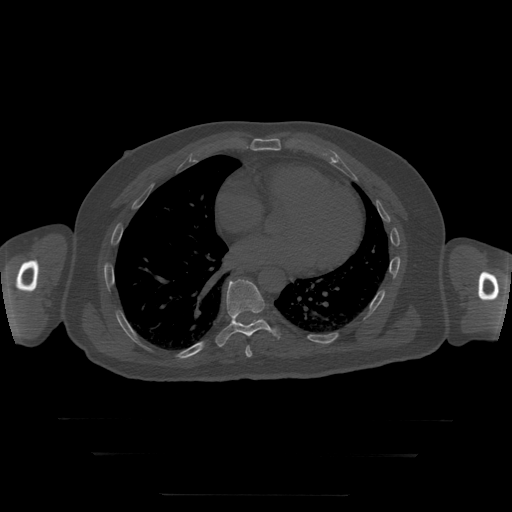
CT including the spine, one axial slice. Slice 145 of 397 in the series (ordered by position). Reconstruction kernel STANDARD. 120 kVp. Bone window (W 1800 / L 400 HU). 512 × 512 image matrix. Patient age 73 years. Case-level facts recorded for this patient, not image findings: primary cancer: prostate.
Annotated regions visible in this slice (semi-automatic segmentation, software-assisted and operator-edited):
- T8 vertebra: box from (x=246, y=346) to (x=253, y=358) px
- T9 vertebra: (x=216, y=280)–(x=281, y=347)